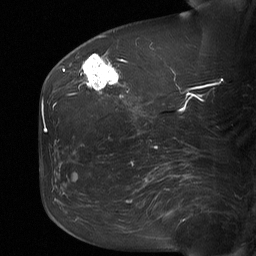
Breast MRI (dynamic contrast-enhanced), one sagittal slice. Position 24 of 64 along the scan axis. Dynamic contrast-enhanced study with each time point stored as its own series, time point 2 of 3 at this slice position (early post-contrast, ordered by acquisition time). 1.5 T. TE 4.8 ms, TR 27 ms. 256 × 256 image matrix, field of view 200 × 200 mm. Patient: female, 60 years. From the clinical record (not read from this slice): setting: breast cancer imaged before/during neoadjuvant chemotherapy; receptor status: HR-positive, HER2-negative.
Annotated regions visible in this slice (semi-automatic segmentation, software-assisted and operator-edited):
- analysis volume of interest (the breast-tissue region the enhancement analysis was run in; not a lesion): bounding box (x1, y1, x2, y2) in pixels: (79, 51, 122, 98)
- tumour enhancement mask (voxels above the 90 % enhancement threshold inside the analysis volume of interest): (83, 54, 119, 90)